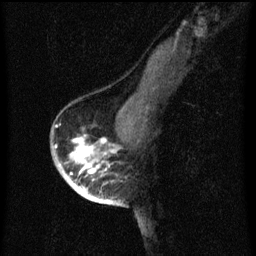
Breast MRI (dynamic contrast-enhanced), one sagittal slice. Position 42 of 60 along the scan axis. Dynamic contrast-enhanced series, image 2 of 3 at this slice position (ordered by acquisition). 1.5 T. TE 4.2 ms, TR 8 ms. 2 mm slice thickness. 256 × 256 image matrix. Patient: female, 56 years.
Structures marked on this image (semi-automatically segmented with operator editing):
- analysis volume of interest (the breast-tissue region the enhancement analysis was run in; not a lesion): bounding box <54,122,120,199> (left, top, right, bottom; pixels)
- tumour enhancement mask (voxels above the 70 % enhancement threshold inside the analysis volume of interest): <54,126,112,199>